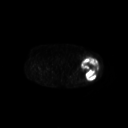
FDG PET of an extremity soft-tissue mass (from a PET/CT study), one axial slice; position 233 of 267 along the scan axis; 128 × 128 image matrix. Patient: female, 62 years. Case-level facts recorded for this patient, not image findings: histological type: undifferentiated – high grade; grade: high; site of the primary tumour: left thigh.
Outlined on this slice (expert contour drawn on MRI and transferred to this co-registered scan by the dataset authors):
- gross tumour volume including surrounding oedema: box from (x=81, y=56) to (x=99, y=81) px
- gross tumour volume (mass): (x=81, y=56)–(x=99, y=81)